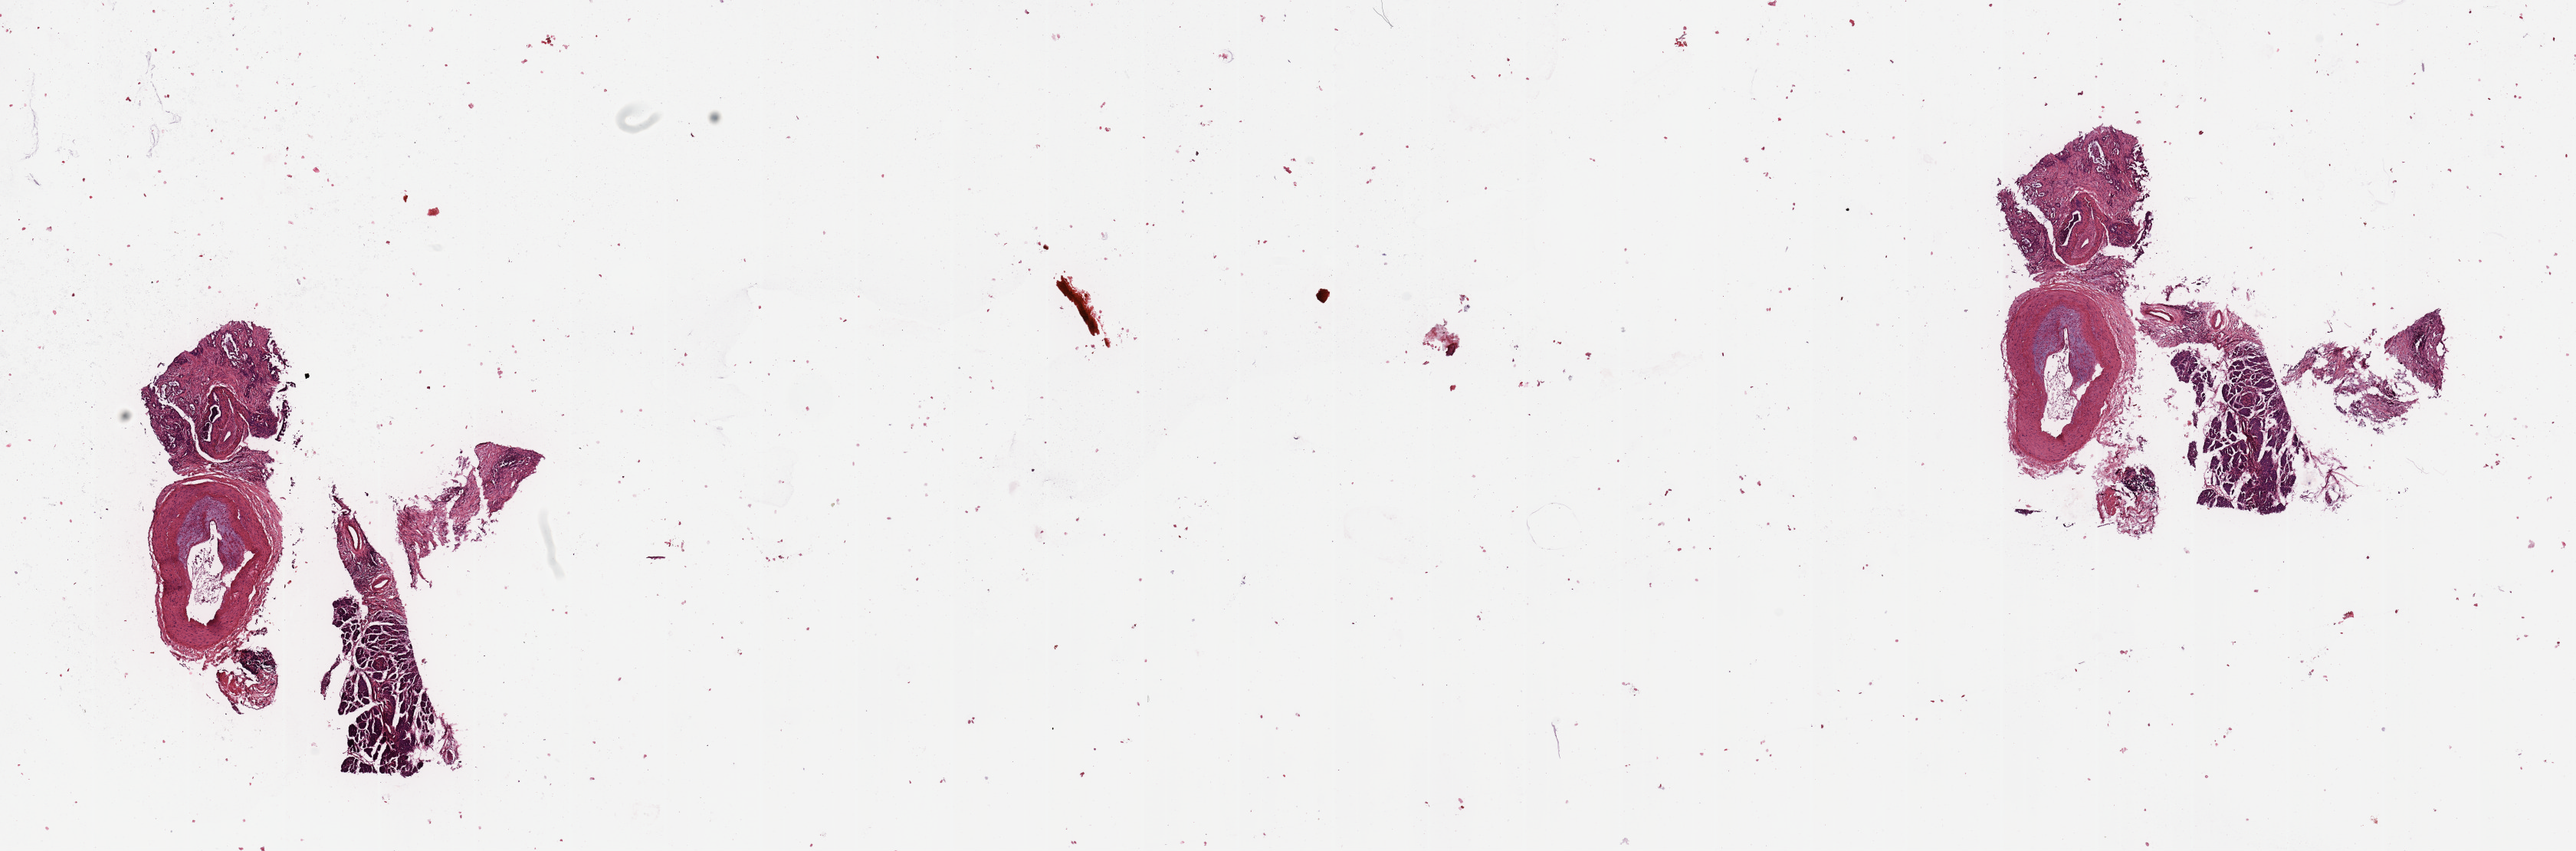
Digitized Hematoxylin and eosin (H&E) stained tissue section (whole slide), whole scanned area (about 26.6 x 8.8 mm) shown as a low-resolution overview. Tumour tissue sample, sampled site: pancreas. Patient: female, age 63 years. Histologic grade: G2 (moderately differentiated). Slide review estimates, as recorded: tumour nuclei 20%, necrosis 3%.
Primary tumour site (as recorded): head. AJCC pathologic stage: III. Histologic diagnosis: Infiltrating duct carcinoma, NOS.